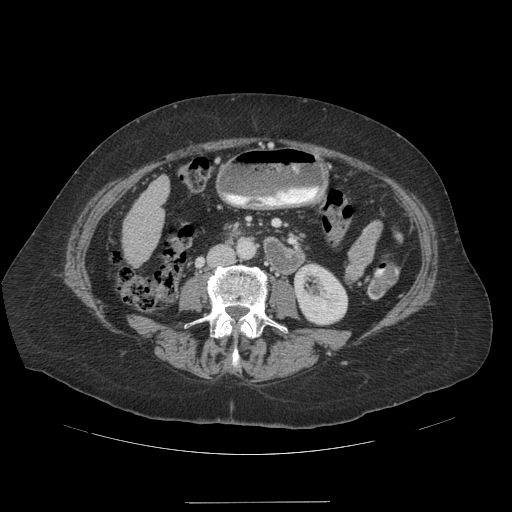
Contrast-enhanced abdominal CT (liver protocol), one axial slice; slice 32 of 99 in the series (ordered by position); soft-tissue window (W 400 / L 40 HU); 512 × 512 image matrix, field of view 440 × 440 mm. Case-level facts recorded for this patient, not image findings: diagnosis: hepatocellular carcinoma (patient treated with transarterial chemoembolisation; whether this scan precedes or follows treatment is not stated here); TNM stage (as recorded): Stage-IVA; Child-Pugh class: A.
Outlined on this slice (semi-automatically segmented with operator editing):
- liver parenchyma outside the tumour (the mass and vessels are separate outlines, so this box may not span the whole liver): bounding box <122,176,168,264> (left, top, right, bottom; pixels)